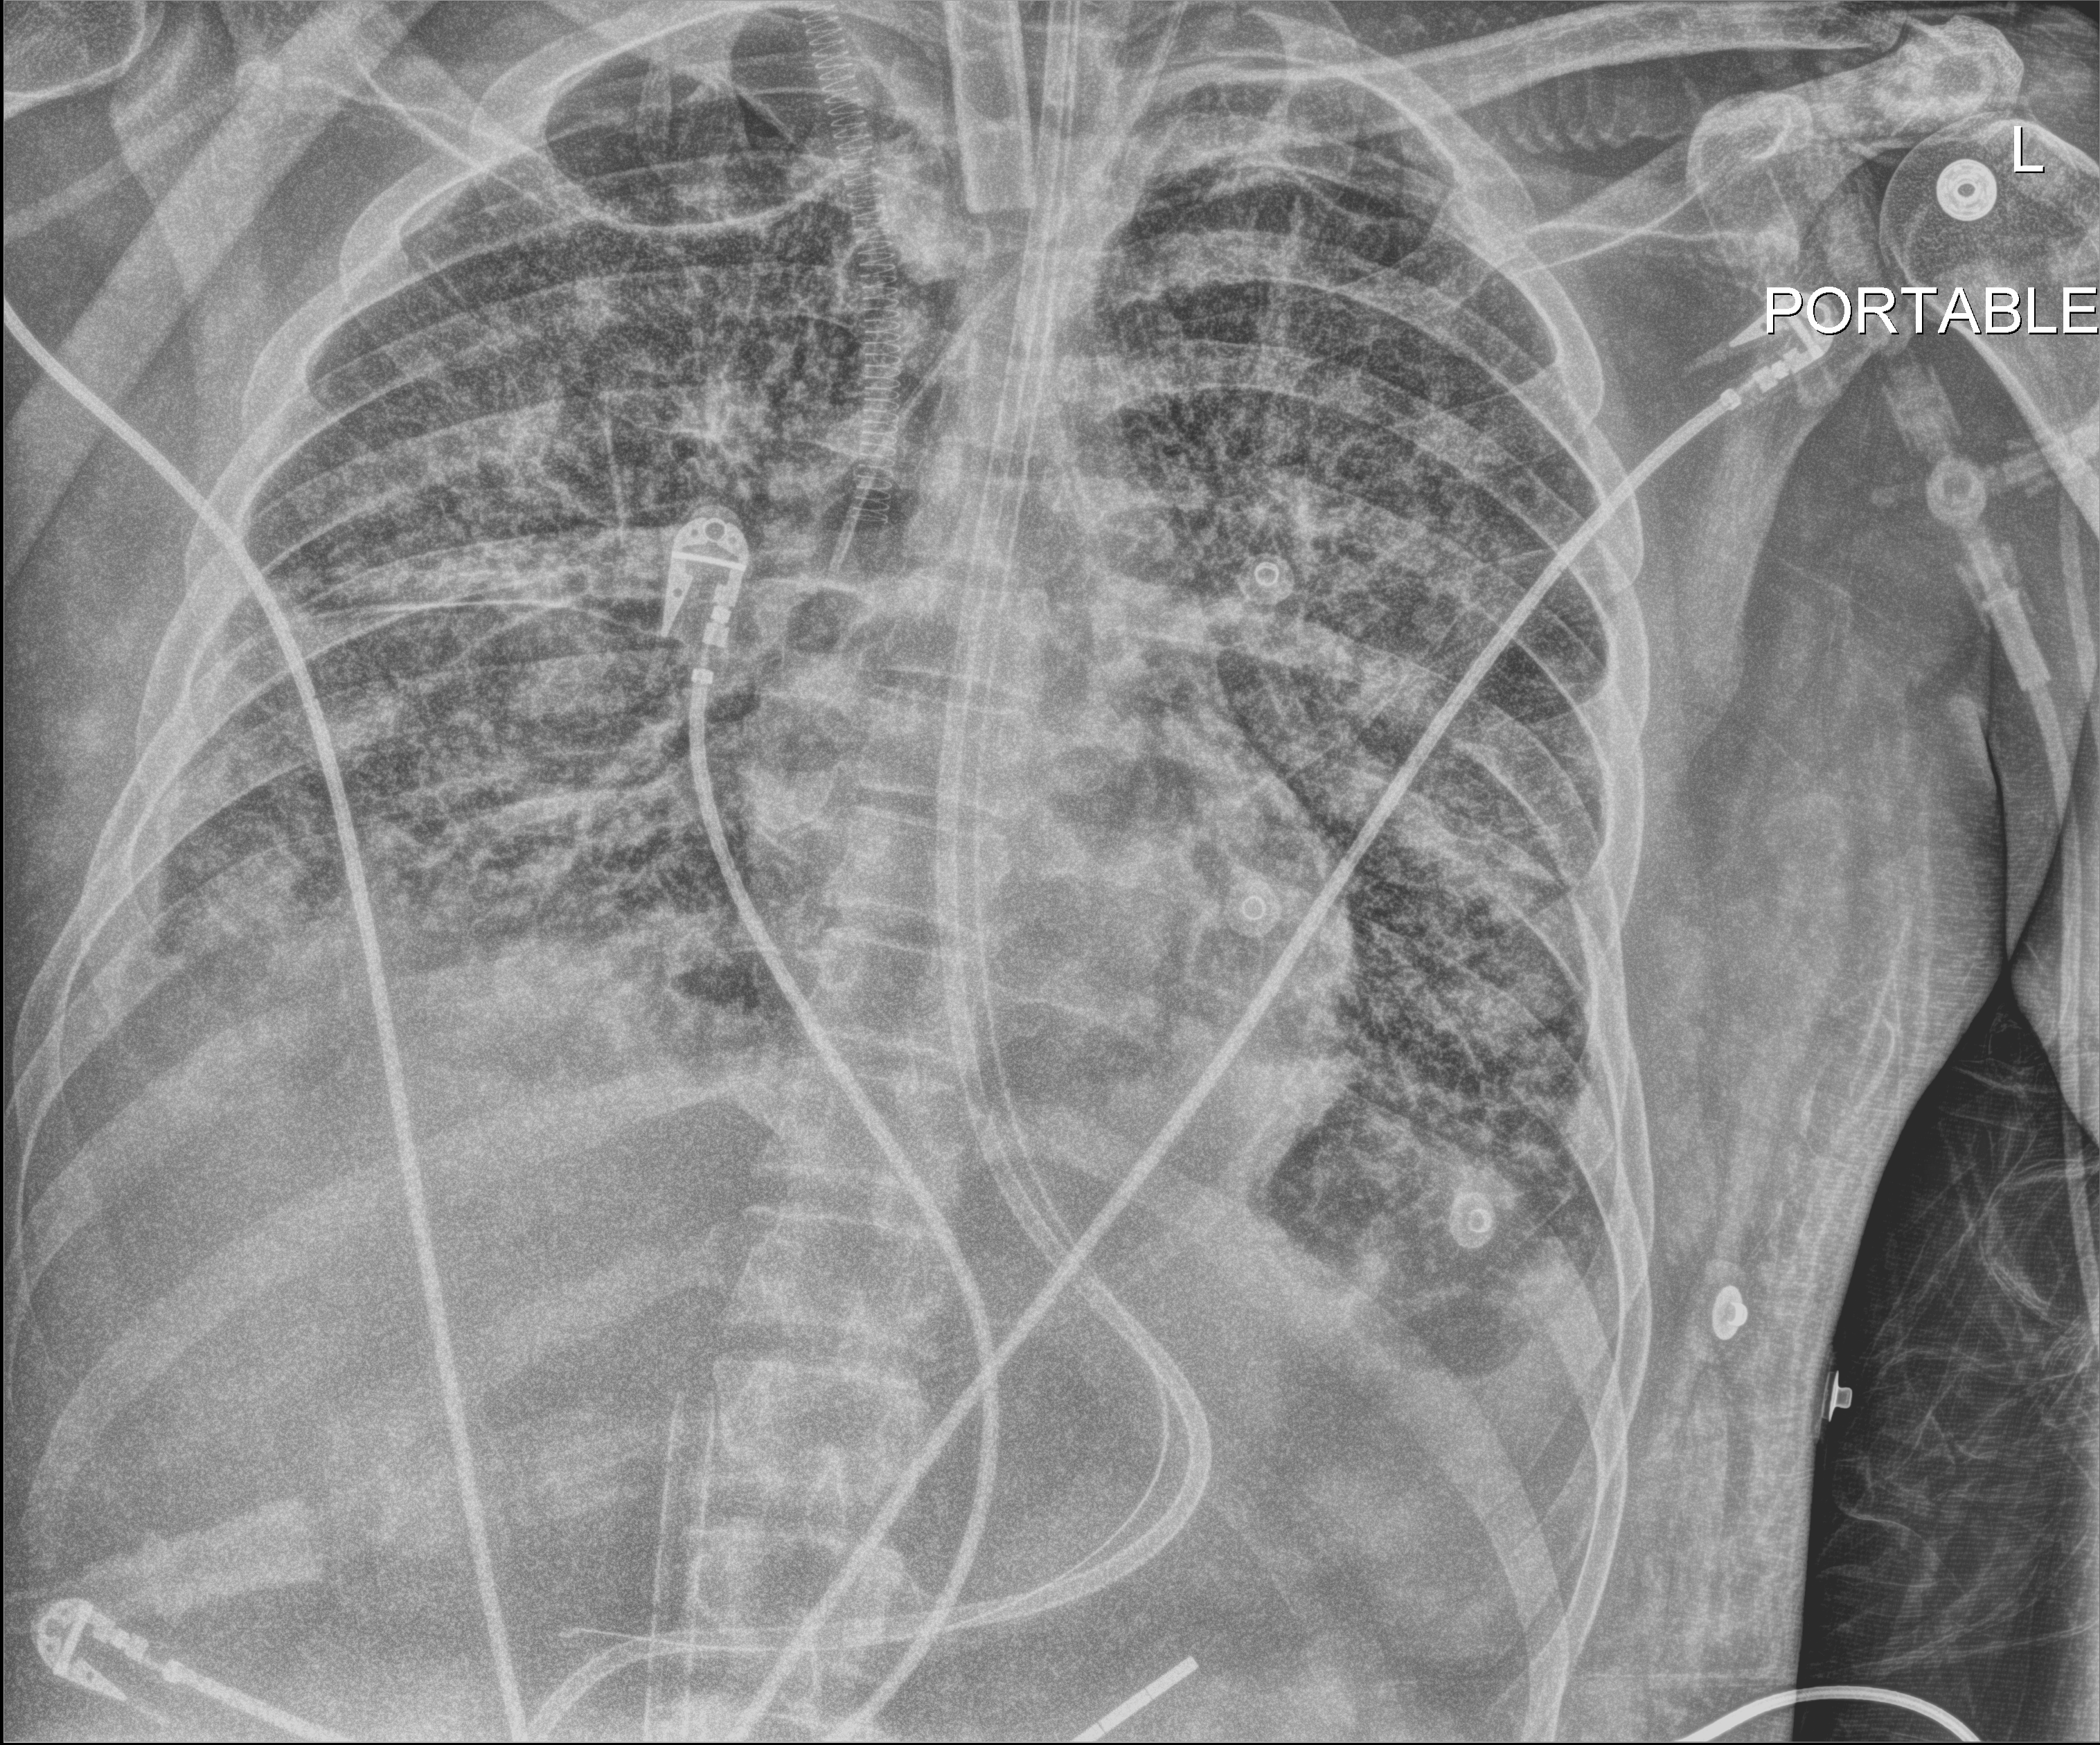
Bedside chest radiograph (digital radiography); anteroposterior (AP) projection. Adult patient hospitalised with COVID-19, age 18–59 years.
Admission-level facts for this patient (not findings on this image; timing relative to this image not recorded):
- mechanically ventilated during this hospital stay: yes
- admitted to intensive care during this hospital stay: yes